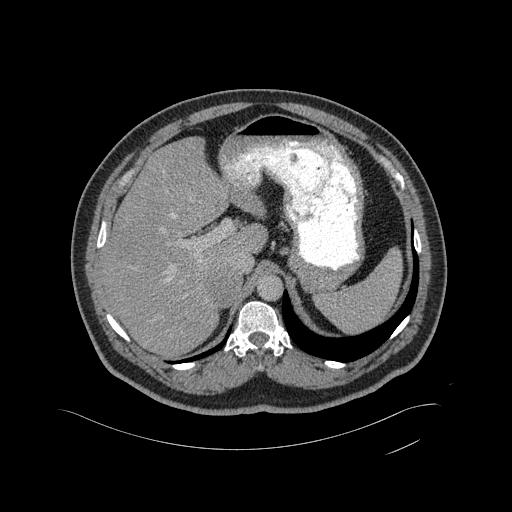
Contrast-enhanced abdominal CT, one axial slice; position 338 of 433 along the scan axis; 120 kVp; intravenous contrast given; soft-tissue window (W 400 / L 40 HU); 512 × 512 image matrix, field of view 500 × 500 mm. Patient: male, 56 years. From the clinical record (not read from this slice): diagnosis: adrenocortical carcinoma; tumour side: right adrenal; tumour size at pathology: 11.6 cm; Ki-67 index: 50 %; stage (as recorded): 3.
Annotated regions visible in this slice (semi-automatically segmented with operator editing):
- mass: bounding box (x1, y1, x2, y2) in pixels: (208, 270, 239, 301)